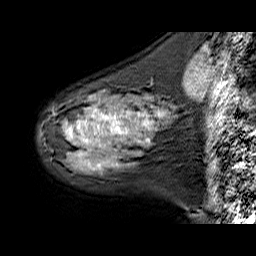
Breast MRI (dynamic contrast-enhanced), one sagittal slice; position 18 of 60 along the scan axis; dynamic contrast-enhanced series, time point 2 of 6 at this slice position (early post-contrast); 1.5 T; TE 6.3 ms, TR 32.9 ms; 4 mm slice thickness; 256 × 256 image matrix. Female patient. From the clinical record (not read from this slice): setting: breast cancer imaged before/during neoadjuvant chemotherapy; receptor status: HER2-positive.
Outlined on this slice (semi-automatic segmentation, software-assisted and operator-edited):
- analysis volume of interest (the breast-tissue region the enhancement analysis was run in; not a lesion): bounding box (x1, y1, x2, y2) in pixels: (40, 79, 177, 173)
- tumour enhancement mask (voxels above the 100 % enhancement threshold inside the analysis volume of interest): (69, 113, 164, 167)